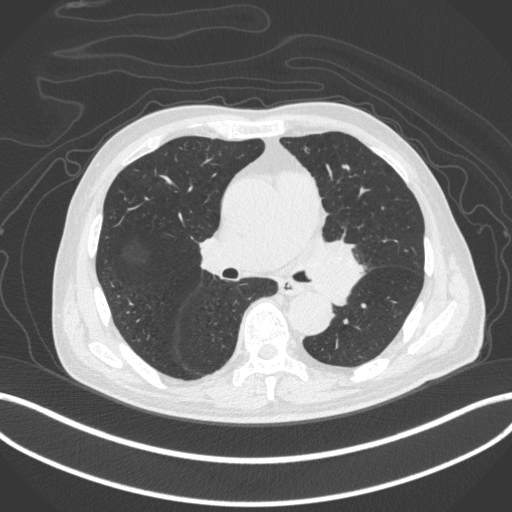
Chest CT, one axial slice; position 245 of 420 along the scan axis; reconstruction kernel B31f; lung window (W 1500 / L -600 HU); 1 mm slice thickness; 512 × 512 image matrix, field of view 400 × 400 mm. Male patient, age 77 years. From the clinical record (not read from this slice): clinical TNM (as recorded): T3 N1 M0.
Outlined on this slice (bounding box drawn by a radiologist):
- lung tumour (recorded histology: adenocarcinoma): bounding box (x1, y1, x2, y2) in pixels: (302, 237, 364, 309)